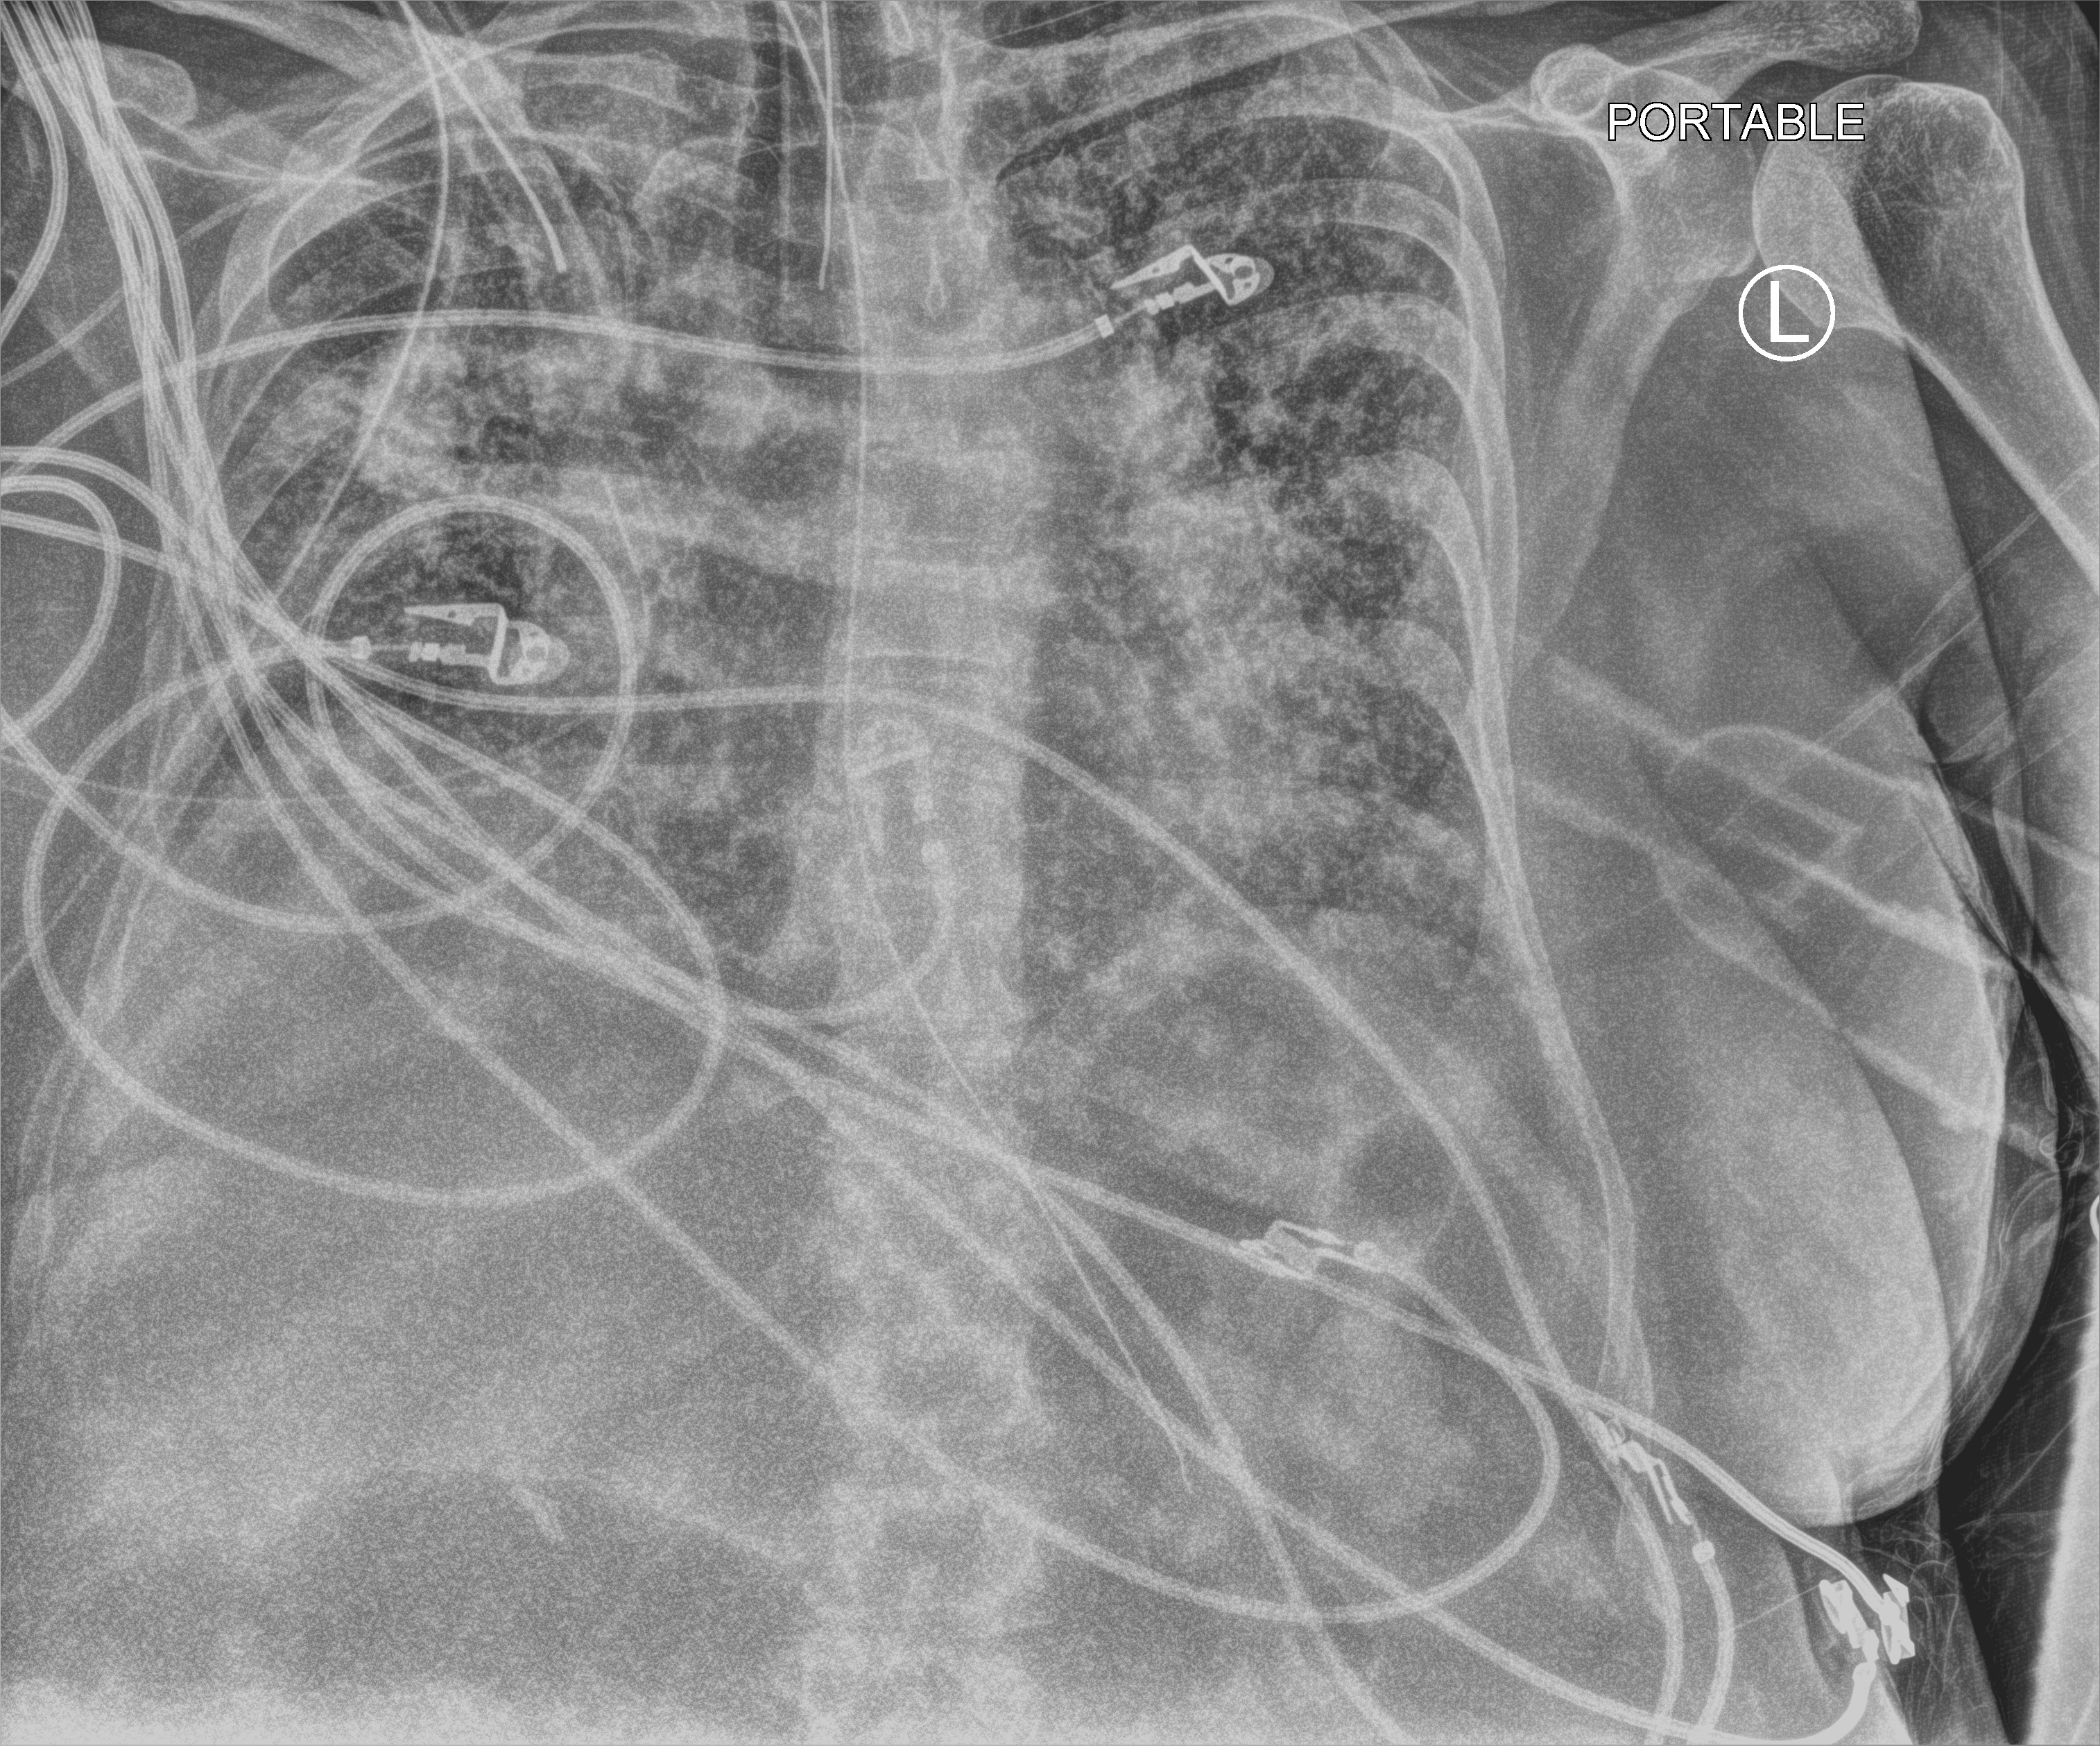
Bedside chest radiograph (computed radiography); anteroposterior (AP) projection. Patient hospitalised with COVID-19; female, aged 60–74 years.
Admission-level facts for this patient (not findings on this image; timing relative to this image not recorded): mechanically ventilated during this hospital stay: yes; length of hospital stay: 45 days.